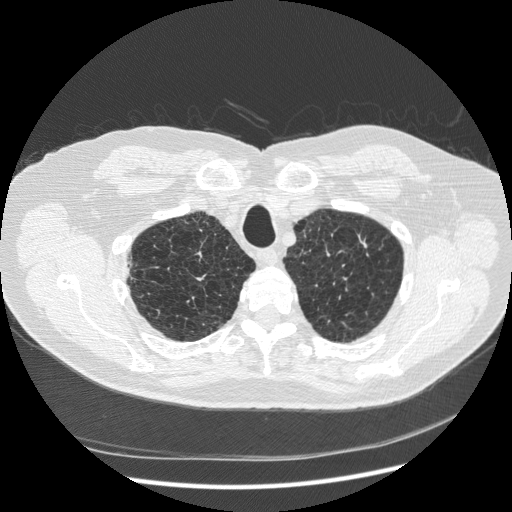
Axial slice from a low-dose chest CT screening exam, baseline annual screen, lung window (W 1500 / L -600 HU), 1.25 mm slice thickness, slice 41 of 265 in the series. Male participant, aged 70 years at enrolment.
- Lesion marked by an expert reader, bounding box <332,218,387,273> (left, top, right, bottom; pixels).
- The screening reader recorded 2 non-calcified nodules or masses ≥4 mm on this exam (right lower lobe, right lower lobe); which of them this box marks is not recorded.
- Official screen result: positive, change unspecified: nodule(s) >= 4 mm or enlarging nodule(s), mass(es), or other non-specific abnormalities suspicious for lung cancer.
- Later outcome: lung cancer diagnosed 816 days after this screen (after the third annual screen) — squamous cell carcinoma, NOS, left upper lobe, moderately differentiated (G2), stage IA (AJCC 6th edition), 18 mm at pathology.